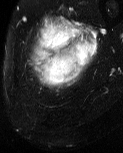
MRI of an extremity soft-tissue mass, one axial slice. T2-weighted fat-saturated. MR volume resampled by the dataset authors to the PET/CT grid (not the native acquisition matrix). 3.27 mm slice thickness. 123 × 153 image matrix, field of view 120 × 149 mm. Male patient. From the clinical record (not read from this slice): histological type: pleiomorphic liposarcoma; grade: high; site of the primary tumour: left thigh.
Annotated regions visible in this slice (expert contour drawn on MRI and transferred to this co-registered scan by the dataset authors):
- gross tumour volume including surrounding oedema: bounding box [x1, y1, x2, y2] px = [31, 15, 98, 89]
- gross tumour volume (mass): [43, 59, 78, 83]